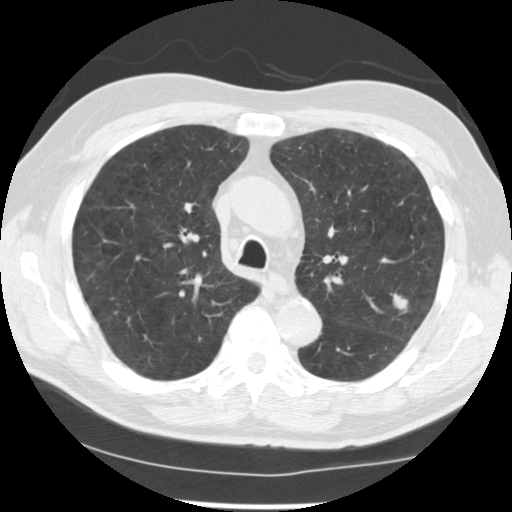
Low-dose screening chest CT, one axial slice. Position 169 of 249 along the scan axis. Reconstruction kernel STANDARD. Lung window (W 1500 / L -600 HU). 2.5 mm slice thickness. 512 × 512 image matrix, field of view 341 × 341 mm.
Outlined on this slice (manually delineated by an expert):
- lesion 1 (tumor, upper lobe of left lung): bounding box <394,295,408,311> (left, top, right, bottom; pixels)